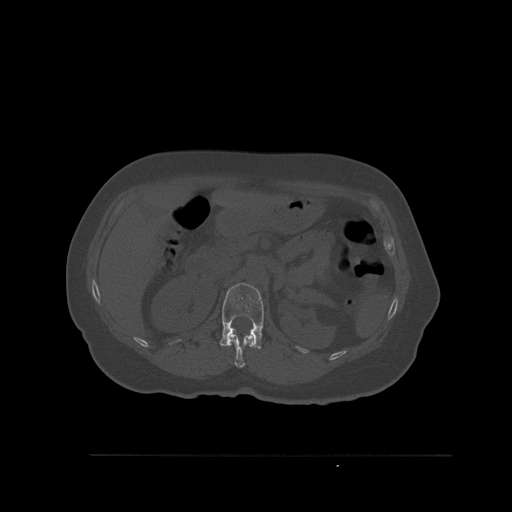
CT including the spine, one axial slice; slice 271 of 527 in the series (ordered by position); bone window (W 1800 / L 400 HU); 1.5 mm slice thickness; 512 × 512 image matrix. Female patient, age 73 years. Case-level facts recorded for this patient, not image findings: primary cancer: breast; vertebrae with lytic lesions (as recorded): L2.
Structures marked on this image (semi-automatic segmentation, software-assisted and operator-edited):
- L1 vertebra: bounding box (x1, y1, x2, y2) in pixels: (219, 283, 264, 349)
- T12 vertebra: (227, 332, 254, 368)